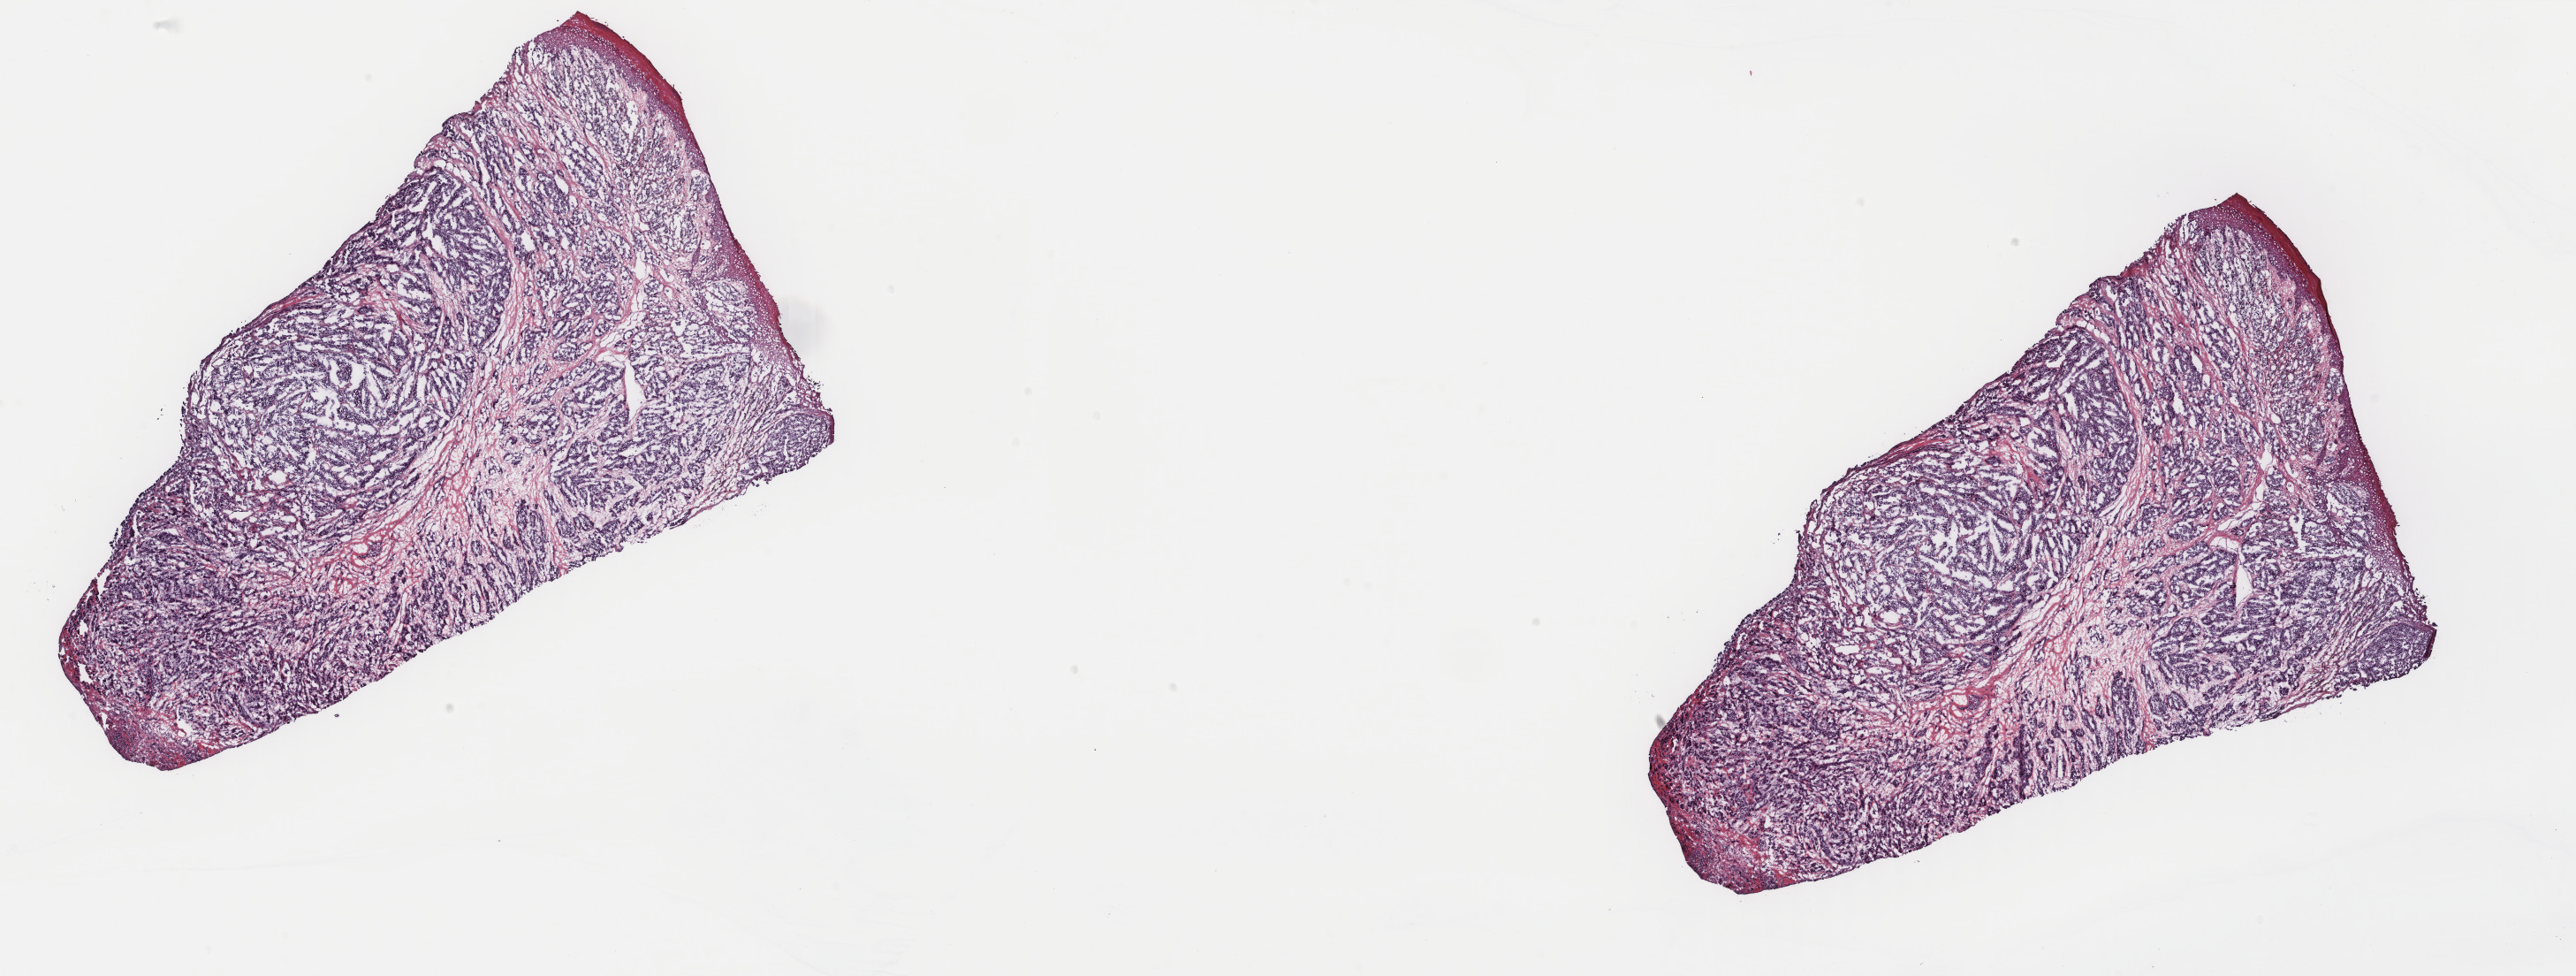
Whole-slide histology image, H&E, whole scanned area (about 23.1 x 8.8 mm) shown as a low-resolution overview. Frozen section. Primary tumour sample from the skin. Patient: male, age at initial diagnosis 43 years. Slide review estimates, as recorded: tumour cells 100%, tumour nuclei 95%.
Diagnosis: Malignant melanoma, NOS.